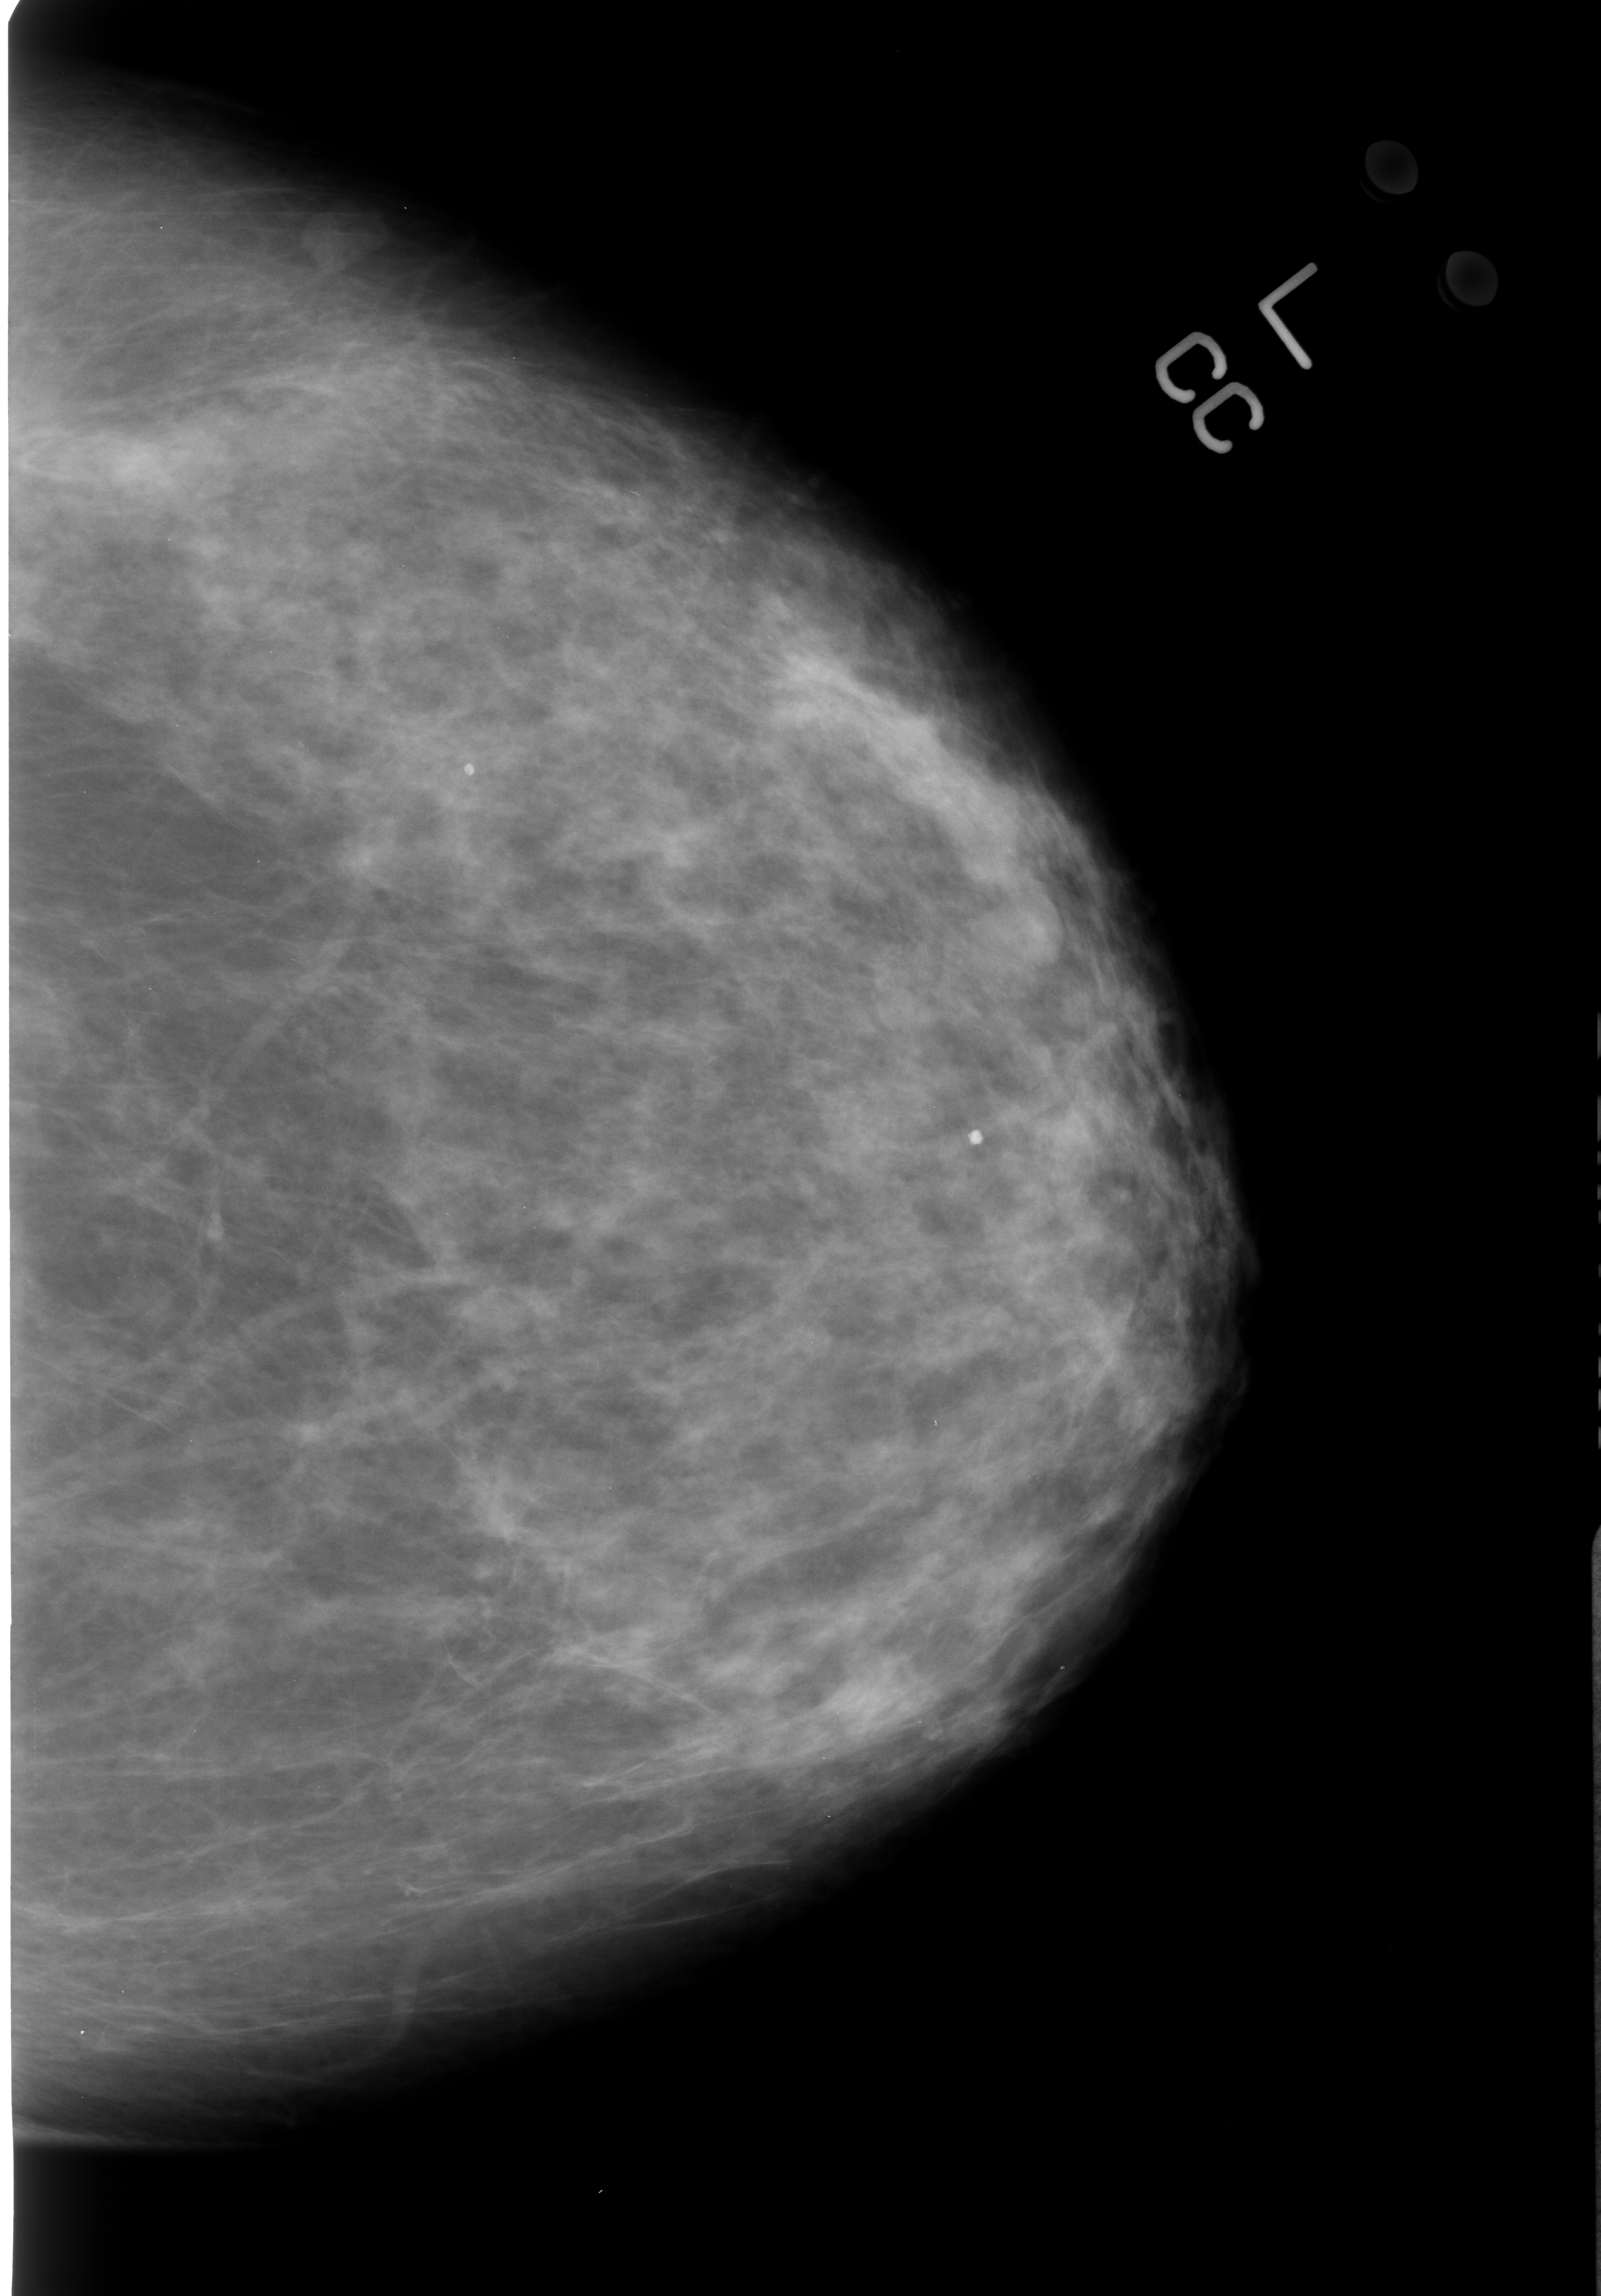
Digitized screen-film mammogram; left breast; craniocaudal (CC) view; breast composition: scattered fibroglandular densities (BI-RADS density category 2 of 4); 1601 × 2296 image matrix.
Expert-marked regions of interest on this image (one box per marked abnormality):
- Finding 1 of 2: calcifications, morphology coarse / round and regular / lucent center; BI-RADS assessment category 2; outcome (as recorded, no biopsy): benign without callback (not worked up further): bounding box (x1, y1, x2, y2) in pixels: (461, 759, 479, 777)
- Finding 2 of 2: calcifications, morphology coarse / round and regular / lucent center; BI-RADS assessment category 2; outcome (as recorded, no biopsy): benign without callback (not worked up further): (963, 1127, 985, 1149)